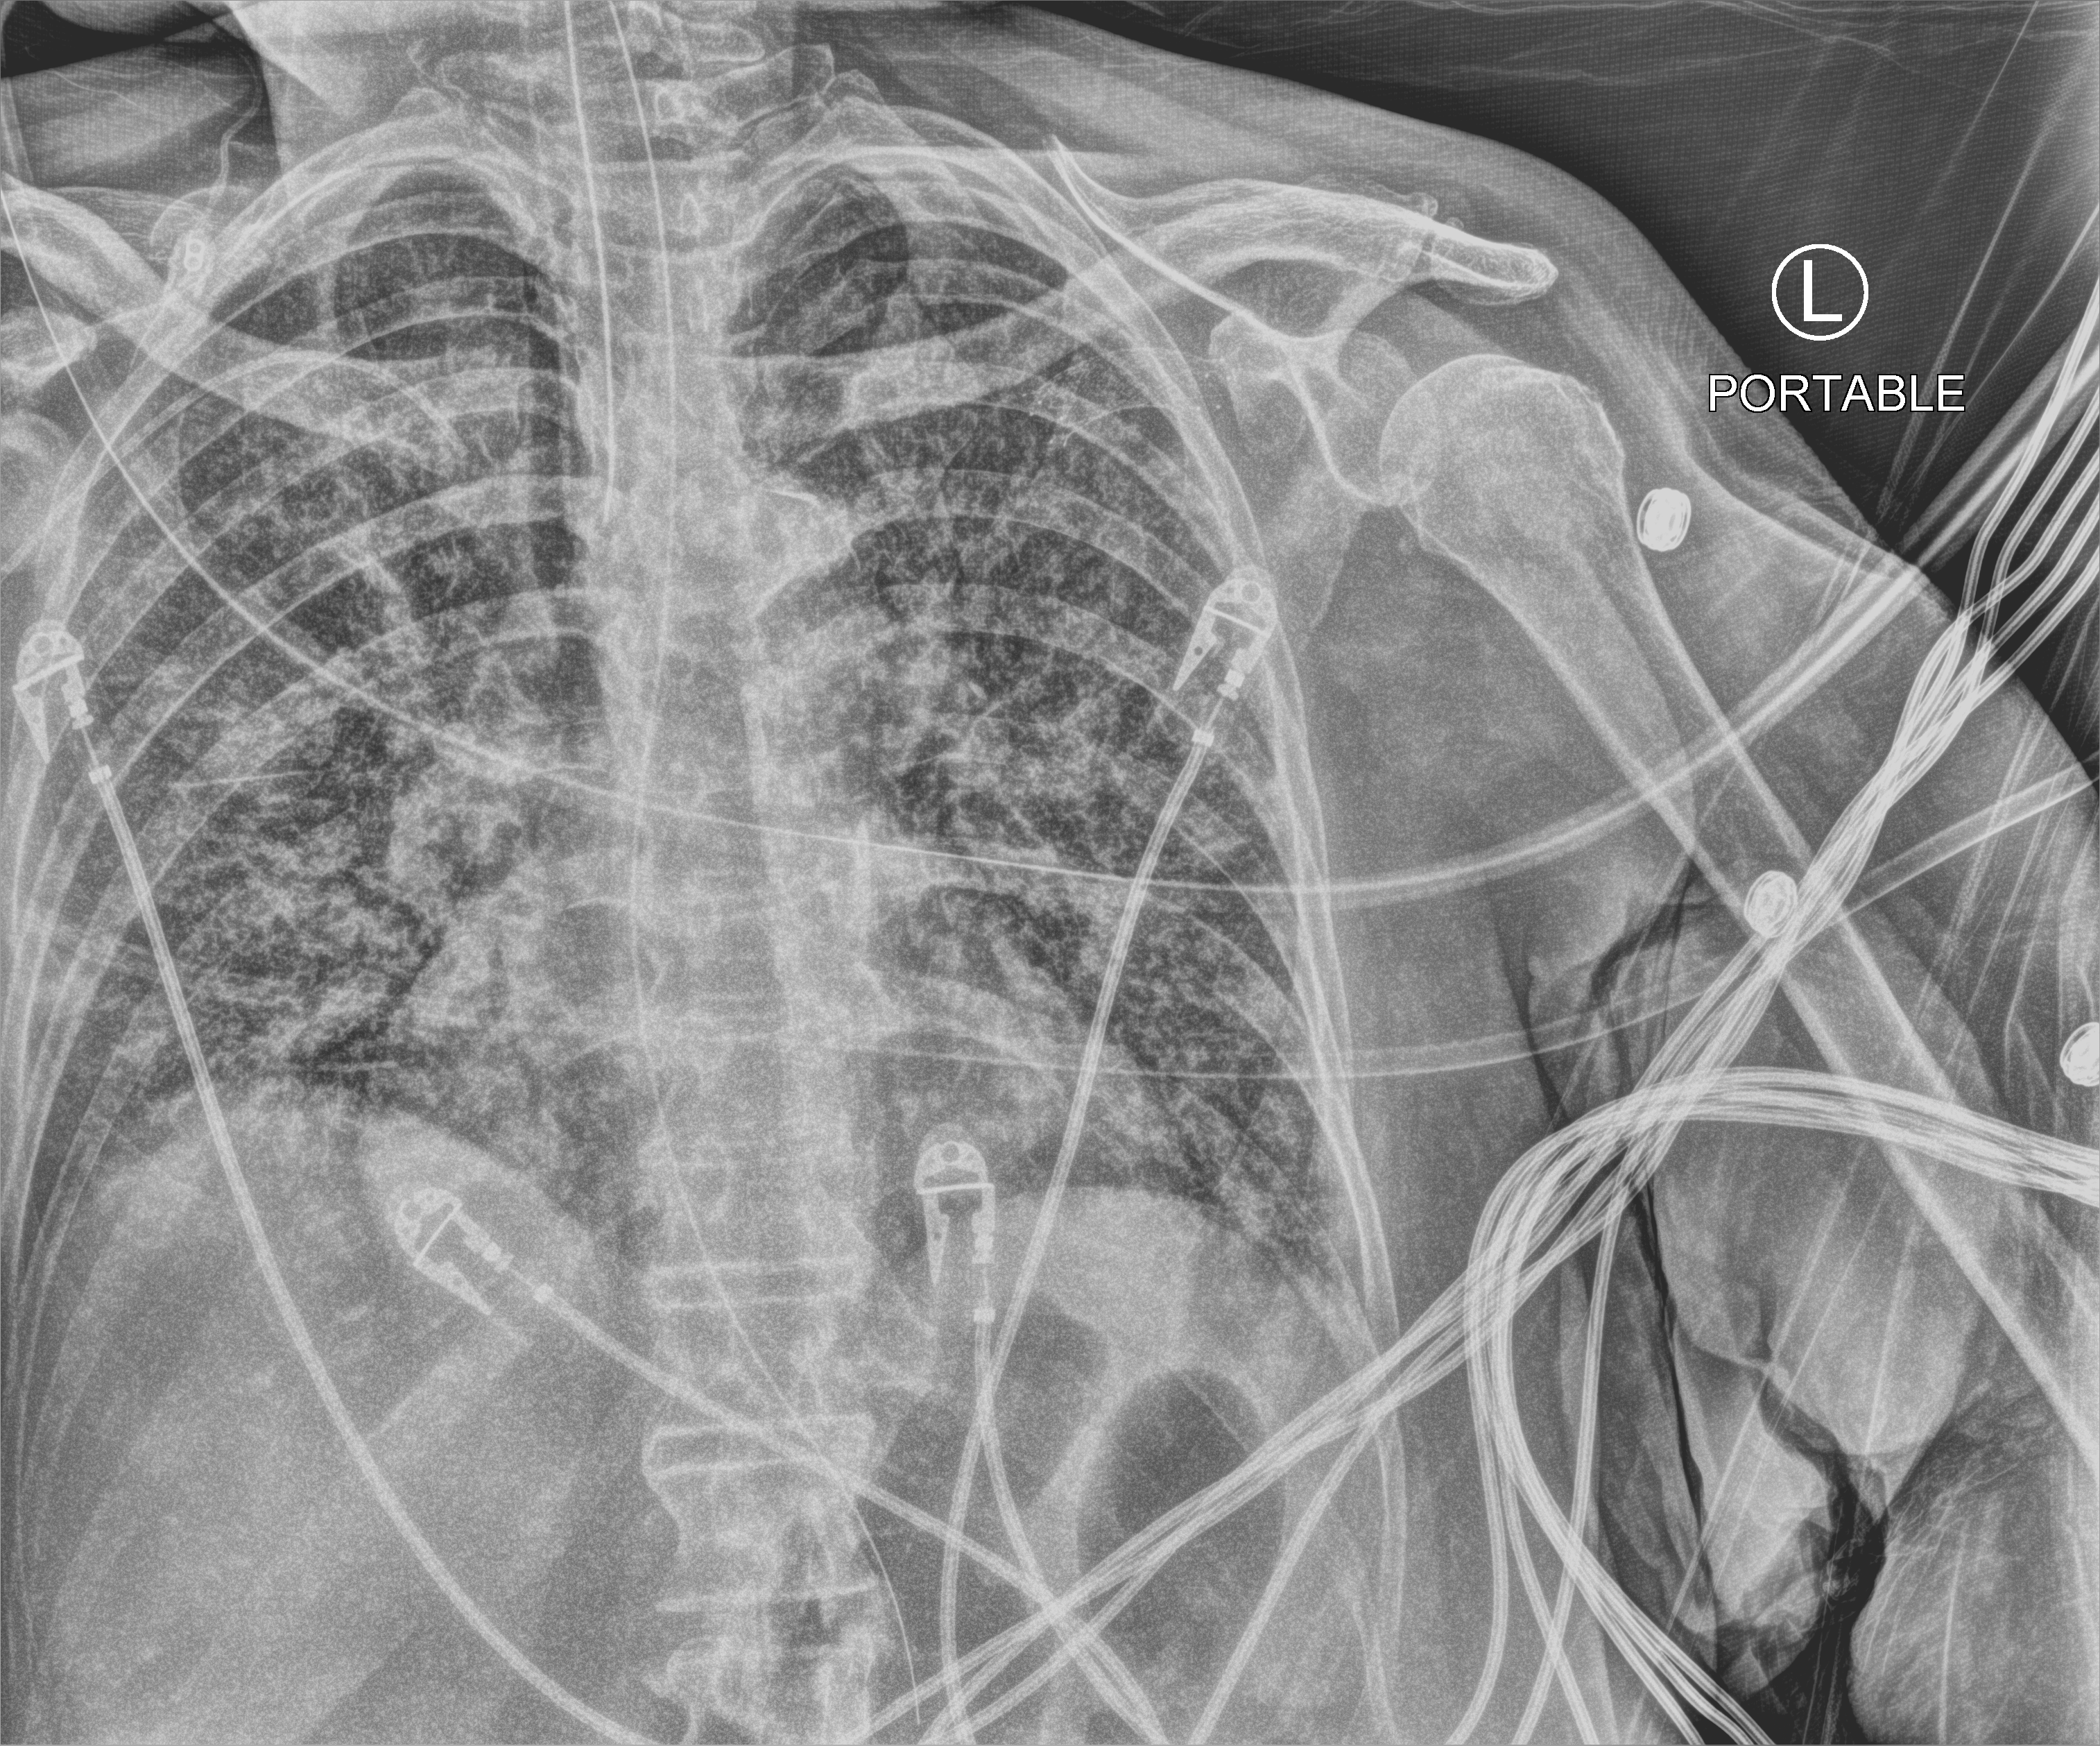
Bedside chest radiograph (computed radiography), anteroposterior (AP) projection. Female patient hospitalised with COVID-19, age 60–74 years.
From the hospital-stay record, not from the radiograph (when in the stay this image was taken is not recorded): admitted to intensive care during this hospital stay: yes.